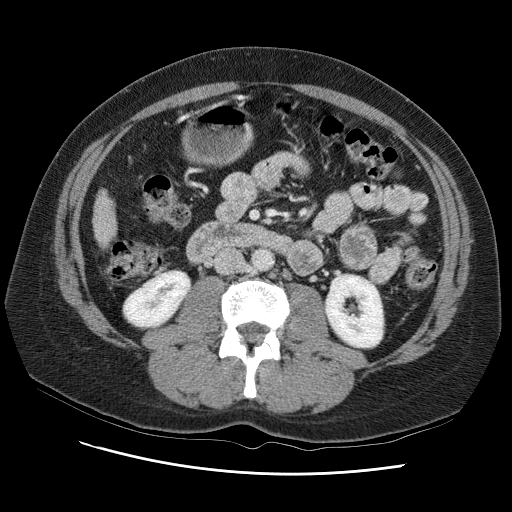
Contrast-enhanced abdominal CT (liver protocol), one axial slice. Position 20 of 95 along the scan axis. Reconstruction kernel STANDARD. 120 kVp. One of 2 acquisitions stored at this slice position. Soft-tissue window (W 400 / L 40 HU). 2.5 mm slice thickness. 512 × 512 image matrix, field of view 360 × 360 mm. From the clinical record (not read from this slice): diagnosis: hepatocellular carcinoma (patient treated with transarterial chemoembolisation; whether this scan precedes or follows treatment is not stated here); TNM stage (as recorded): Stage-I; Child-Pugh class: B; tumour differentiation: moderately differentiated.
Annotated regions visible in this slice (semi-automatically segmented with operator editing):
- liver parenchyma outside the tumour (the mass and vessels are separate outlines, so this box may not span the whole liver): box from (x=96, y=168) to (x=134, y=252) px
- liver vessels: (x=114, y=217)–(x=122, y=239)